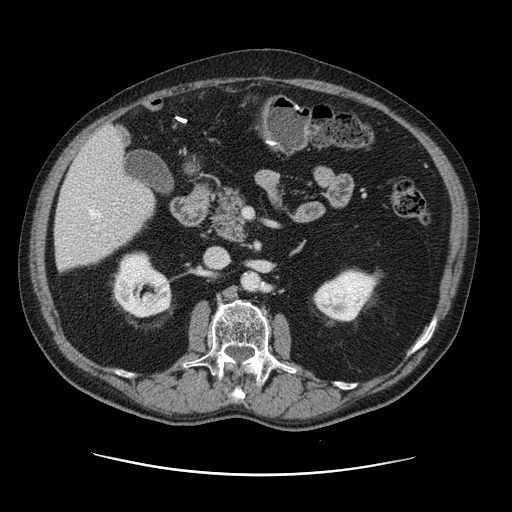
Contrast-enhanced abdominal CT, one axial slice. Slice 55 of 141 in the series (ordered by position). Soft-tissue window (W 400 / L 40 HU). 2.5 mm slice thickness. 512 × 512 image matrix, field of view 395 × 395 mm. Male patient, age 72 years. Case-level facts recorded for this patient, not image findings: diagnosis: colorectal cancer liver metastases, imaged before liver resection; multiple liver metastases: yes; largest metastasis: 5.4 cm; disease in both lobes: yes.
Outlined on this slice (manually delineated by an expert):
- hepatic veins: bounding box <89,209,101,229> (left, top, right, bottom; pixels)
- liver: <56,127,154,270>
- planned liver remnant (the part of the liver to remain after resection): <55,179,154,269>